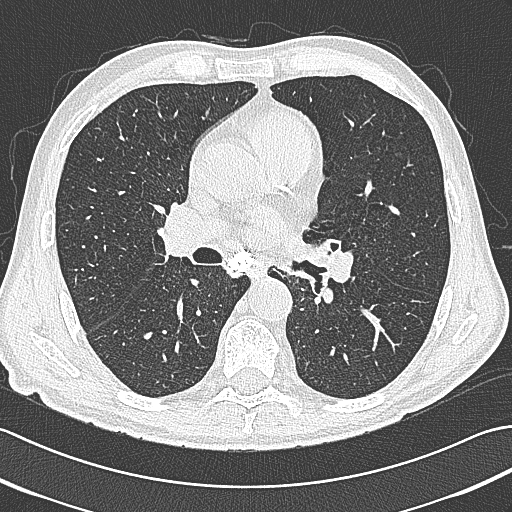
Chest CT (low-dose screening protocol), one axial image. First (baseline) screen. Lung window (W 1500 / L -600 HU). Lung (sharp) reconstruction kernel (B80f). Male, age 65 years at enrolment. Current smoker at enrolment.
Expert reader's lesion annotation, bounding box <304,231,350,276> (left, top, right, bottom; pixels). No non-calcified nodule or mass ≥4 mm was recorded by the screening reader at this exam. Participant outcome: lung cancer diagnosed 161 days after this screen — large cell neuroendocrine carcinoma, left hilum, left main stem bronchus, stage IIIB (AJCC 6th edition), 70 mm at pathology.